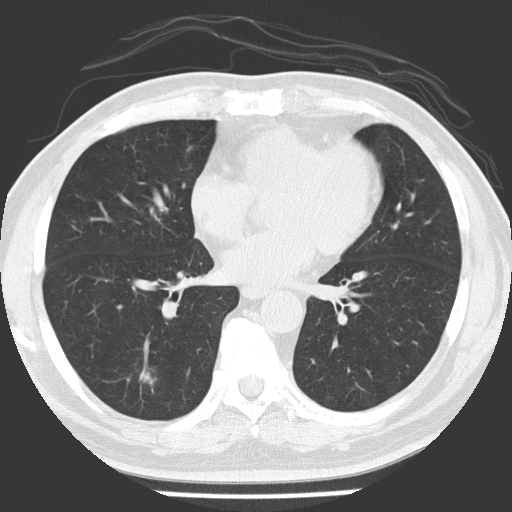
Low-dose screening chest CT, one axial slice. Slice 69 of 154 in the series (ordered by position). Lung window (W 1500 / L -600 HU). 512 × 512 image matrix, field of view 311 × 311 mm.
Structures marked on this image (outlined manually by an expert reader):
- lesion 1 (tumor, lower lobe of right lung): bounding box (x1, y1, x2, y2) in pixels: (140, 367, 153, 392)